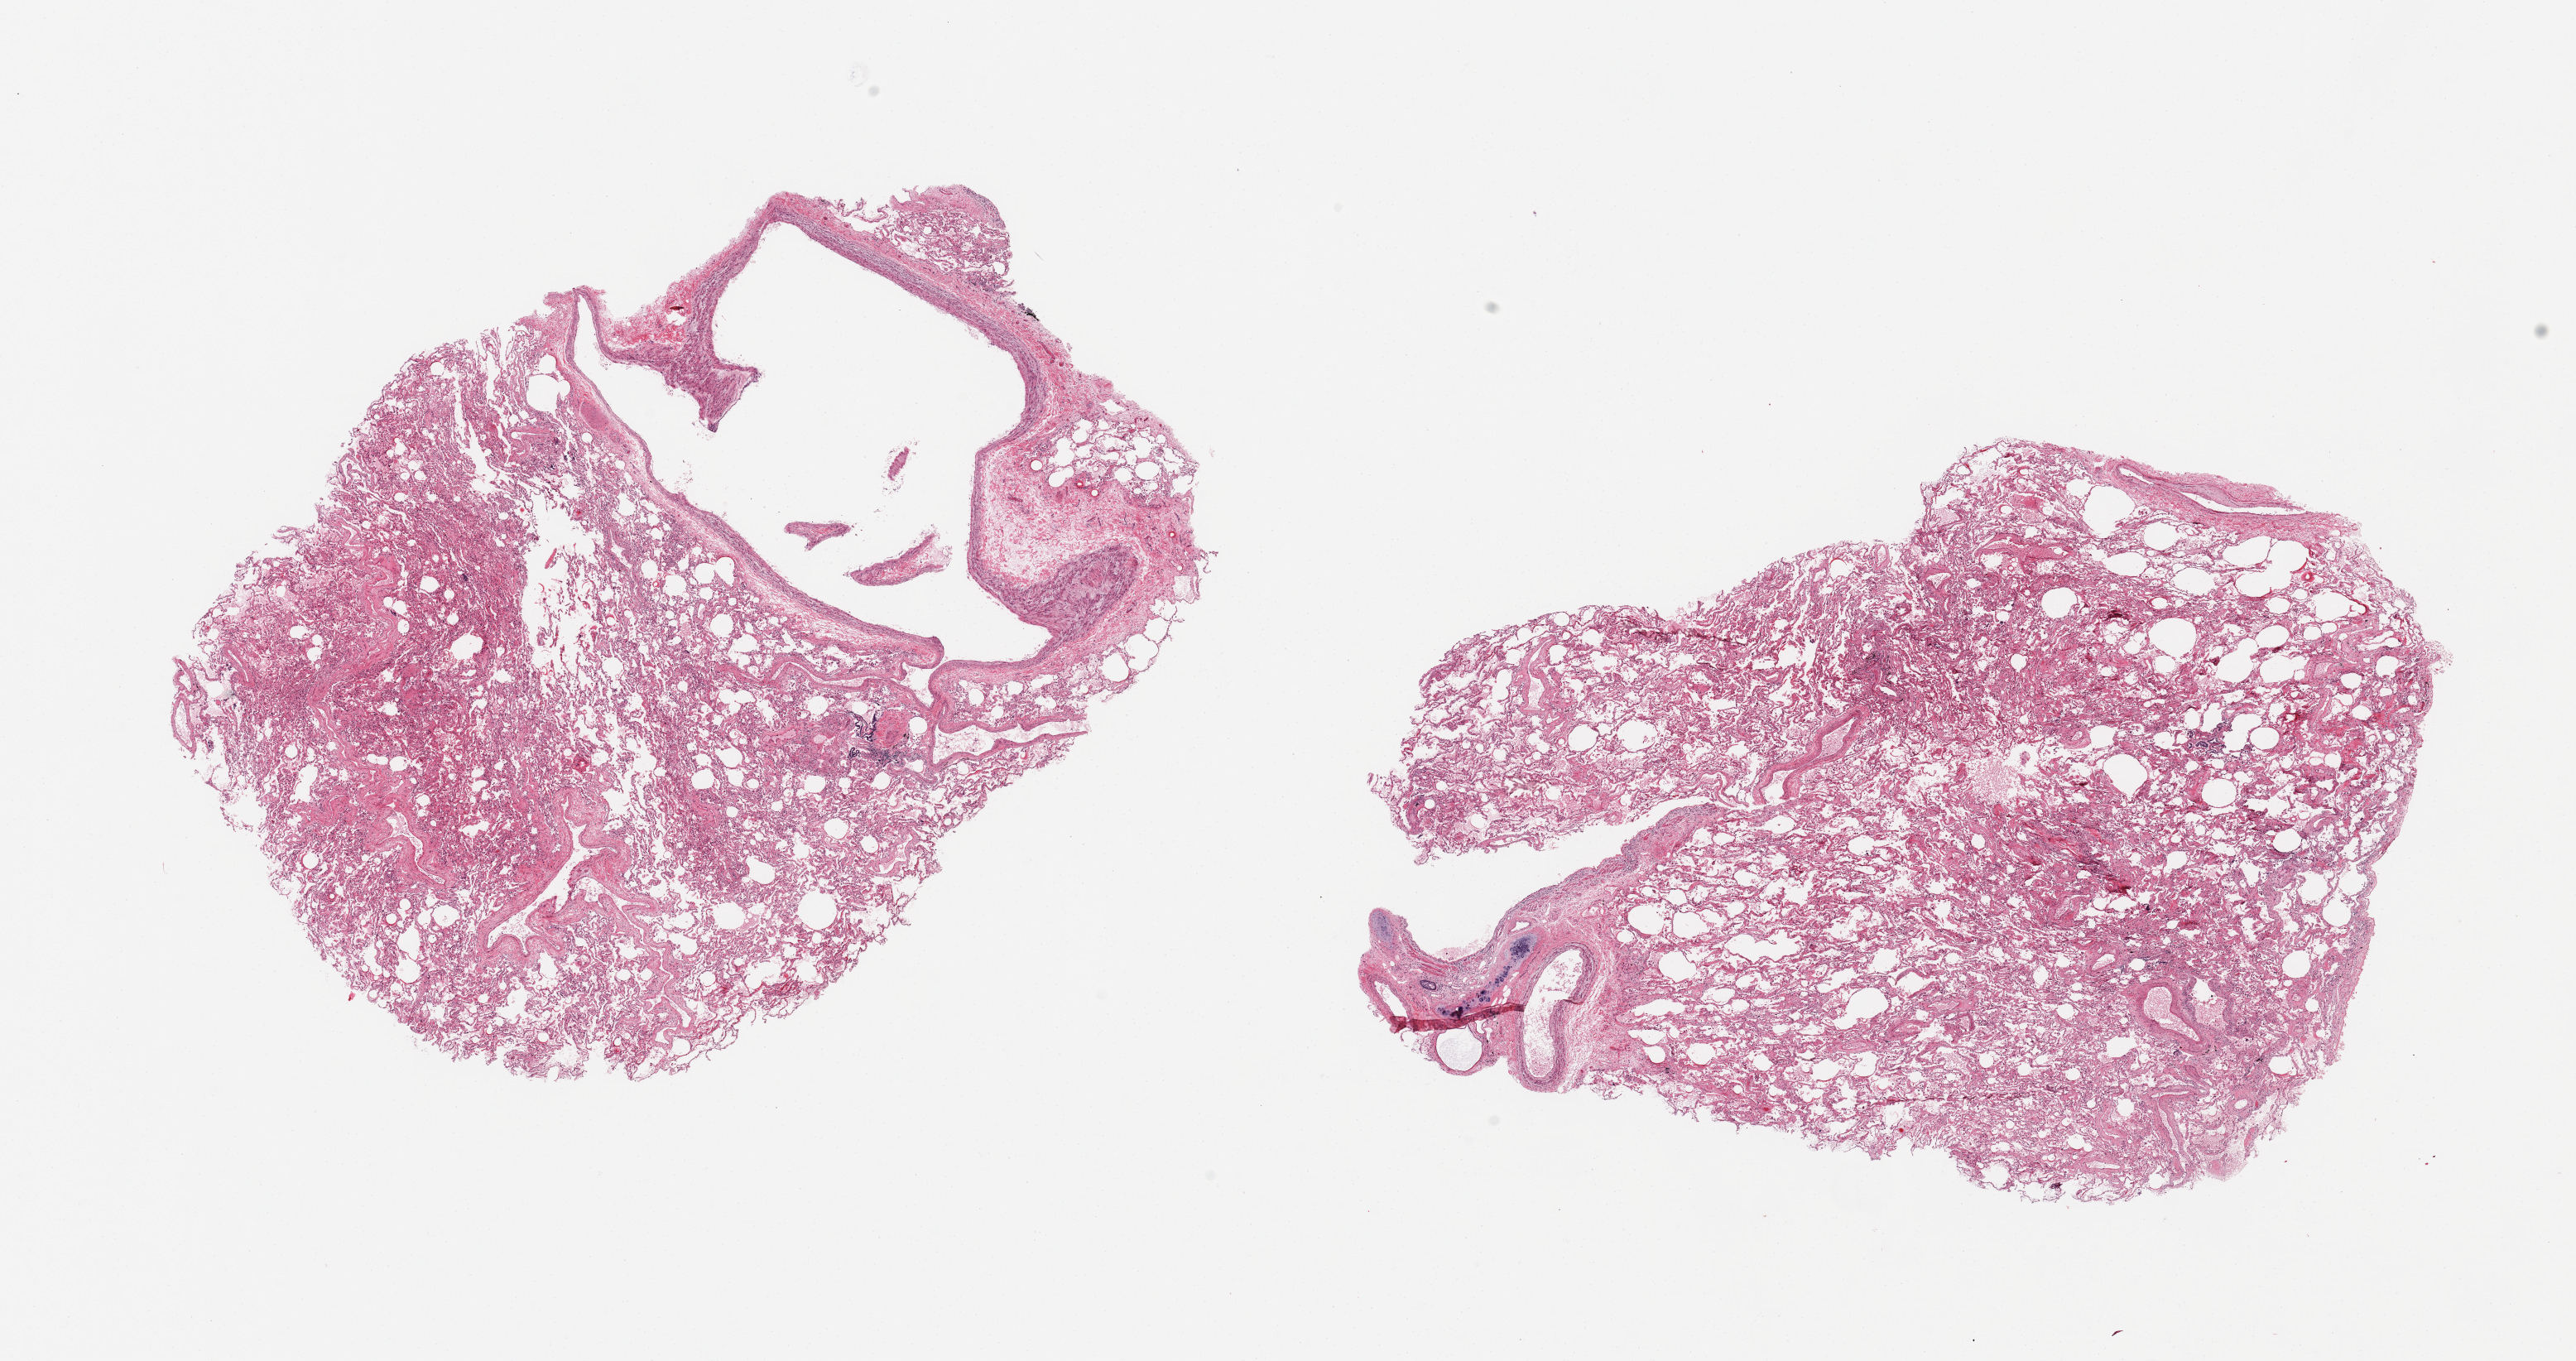
Digitized H&E-stained section, low-resolution overview of the scanned area, about 24.6 x 13.0 mm. PAXgene-fixed, paraffin-embedded tissue. Section of lung (target tissue). Donor tissue sample. Donor: female.
* pathologist's review note for this sample: 2 pieces, mild edema/congestion